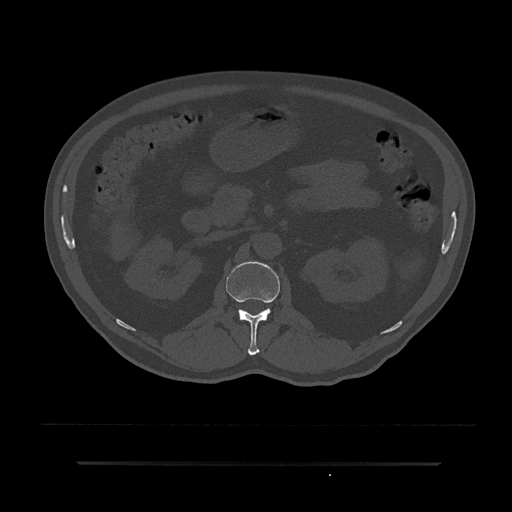
CT including the spine, one axial slice; slice 134 of 797 in the series (ordered by position); 120 kVp; bone window (W 1800 / L 400 HU); 0.5 mm slice thickness; 512 × 512 image matrix, field of view 464 × 464 mm. Patient: male, 59 years. Case-level facts recorded for this patient, not image findings: primary cancer: bile ducts; vertebrae with lytic lesions (as recorded): T10.
Outlined on this slice (semi-automatic segmentation, software-assisted and operator-edited):
- L1 vertebra: bounding box <226,262,280,355> (left, top, right, bottom; pixels)